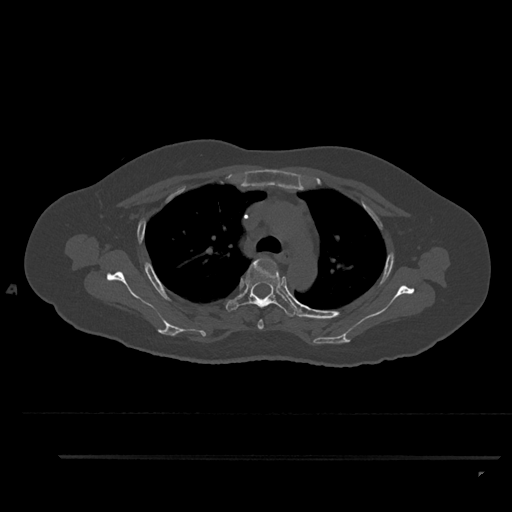
CT including the spine, one axial slice; slice 653 of 797 in the series (ordered by position); reconstruction kernel Br40s/3; bone window (W 1800 / L 400 HU); 0.5 mm slice thickness; 512 × 512 image matrix, field of view 408 × 408 mm. Patient: female, 44 years. Case-level facts recorded for this patient, not image findings: primary cancer: renal; vertebrae with lytic lesions (as recorded): L1.
Structures marked on this image (semi-automatic segmentation, software-assisted and operator-edited):
- T3 vertebra: bounding box <257,319,264,329> (left, top, right, bottom; pixels)
- T4 vertebra: <226,258,296,317>